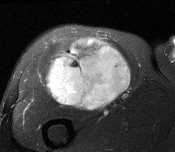
MRI of an extremity soft-tissue mass, one axial slice. Slice 99 of 116 in the series (ordered by position). T2-weighted fat-saturated. MR volume resampled by the dataset authors to the PET/CT grid (not the native acquisition matrix). 3.27 mm slice thickness. 175 × 152 image matrix. Male patient. From the clinical record (not read from this slice): histological type: pleiomorphic leiomyosarcoma; grade: intermediate; site of the primary tumour: right thigh.
Annotated regions visible in this slice (expert contour drawn on MRI and transferred to this co-registered scan by the dataset authors):
- gross tumour volume including surrounding oedema: bounding box [x1, y1, x2, y2] px = [47, 38, 132, 110]
- gross tumour volume (mass): [47, 38, 132, 110]